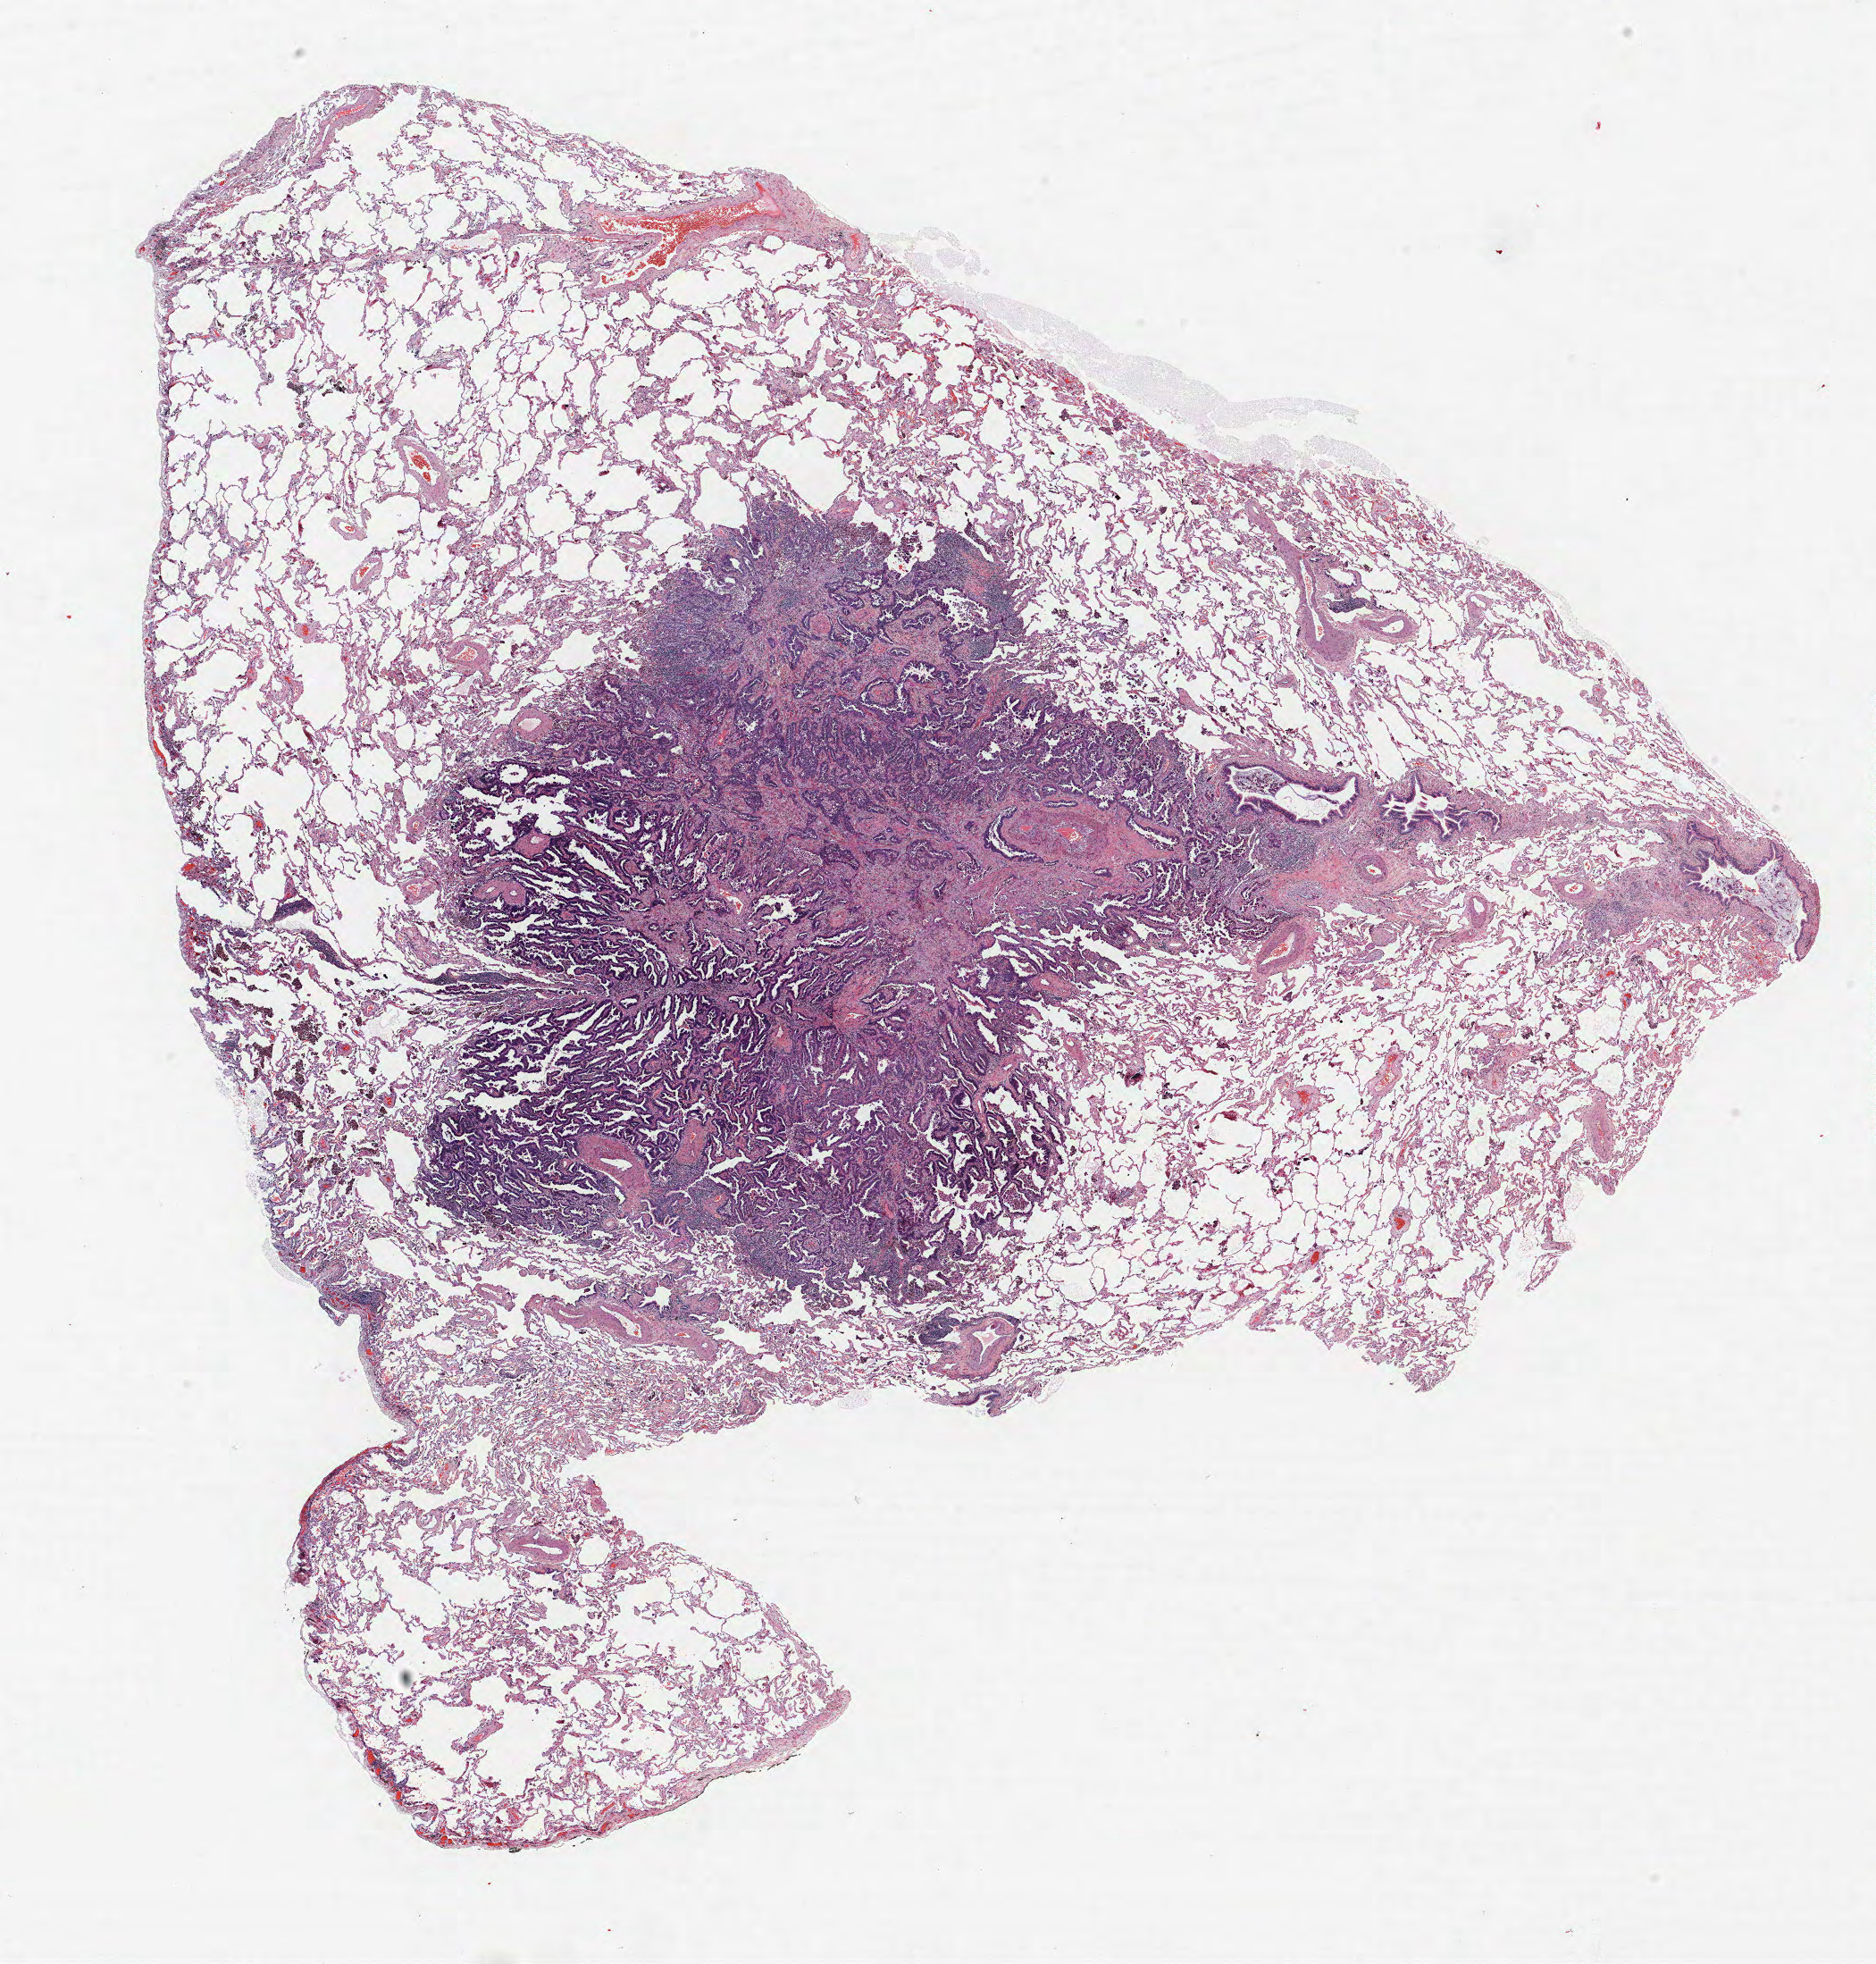
Whole-slide histology image, H&E-stained — low-resolution overview of the scanned area, about 16.8 x 17.6 mm (acquisition: 40x scan), formalin-fixed paraffin-embedded (FFPE) section, lung tissue. Female, age 58 at enrolment. Former smoker at enrolment. Grade: well differentiated (G1).
Participant's lung-cancer diagnosis: Adenocarcinoma, NOS (ICD-O-3 8140/3). Stage (AJCC 6th edition): IB. Primary tumour location (clinical record): right lower lobe. Tumour size (pathology): 10 mm.